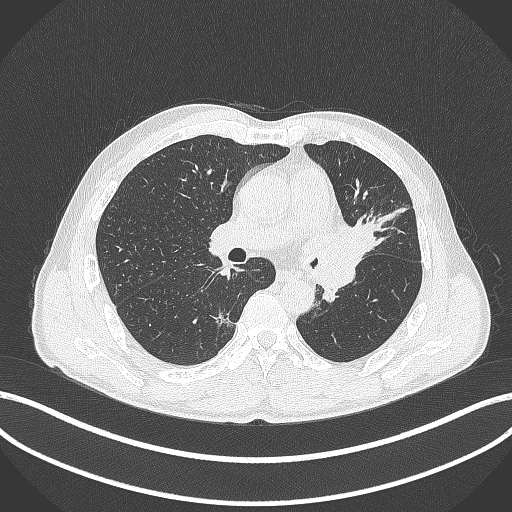
Chest CT, one axial slice; position 237 of 429 along the scan axis; reconstruction kernel B70f; lung window (W 1500 / L -600 HU); 1 mm slice thickness; 512 × 512 image matrix, field of view 400 × 400 mm. Patient: male, 57 years. From the clinical record (not read from this slice): clinical TNM (as recorded): T2b N0 M0.
Outlined on this slice (rectangle marked by the reading radiologist):
- lung tumour (recorded histology: squamous cell carcinoma): box from (x=318, y=222) to (x=383, y=283) px